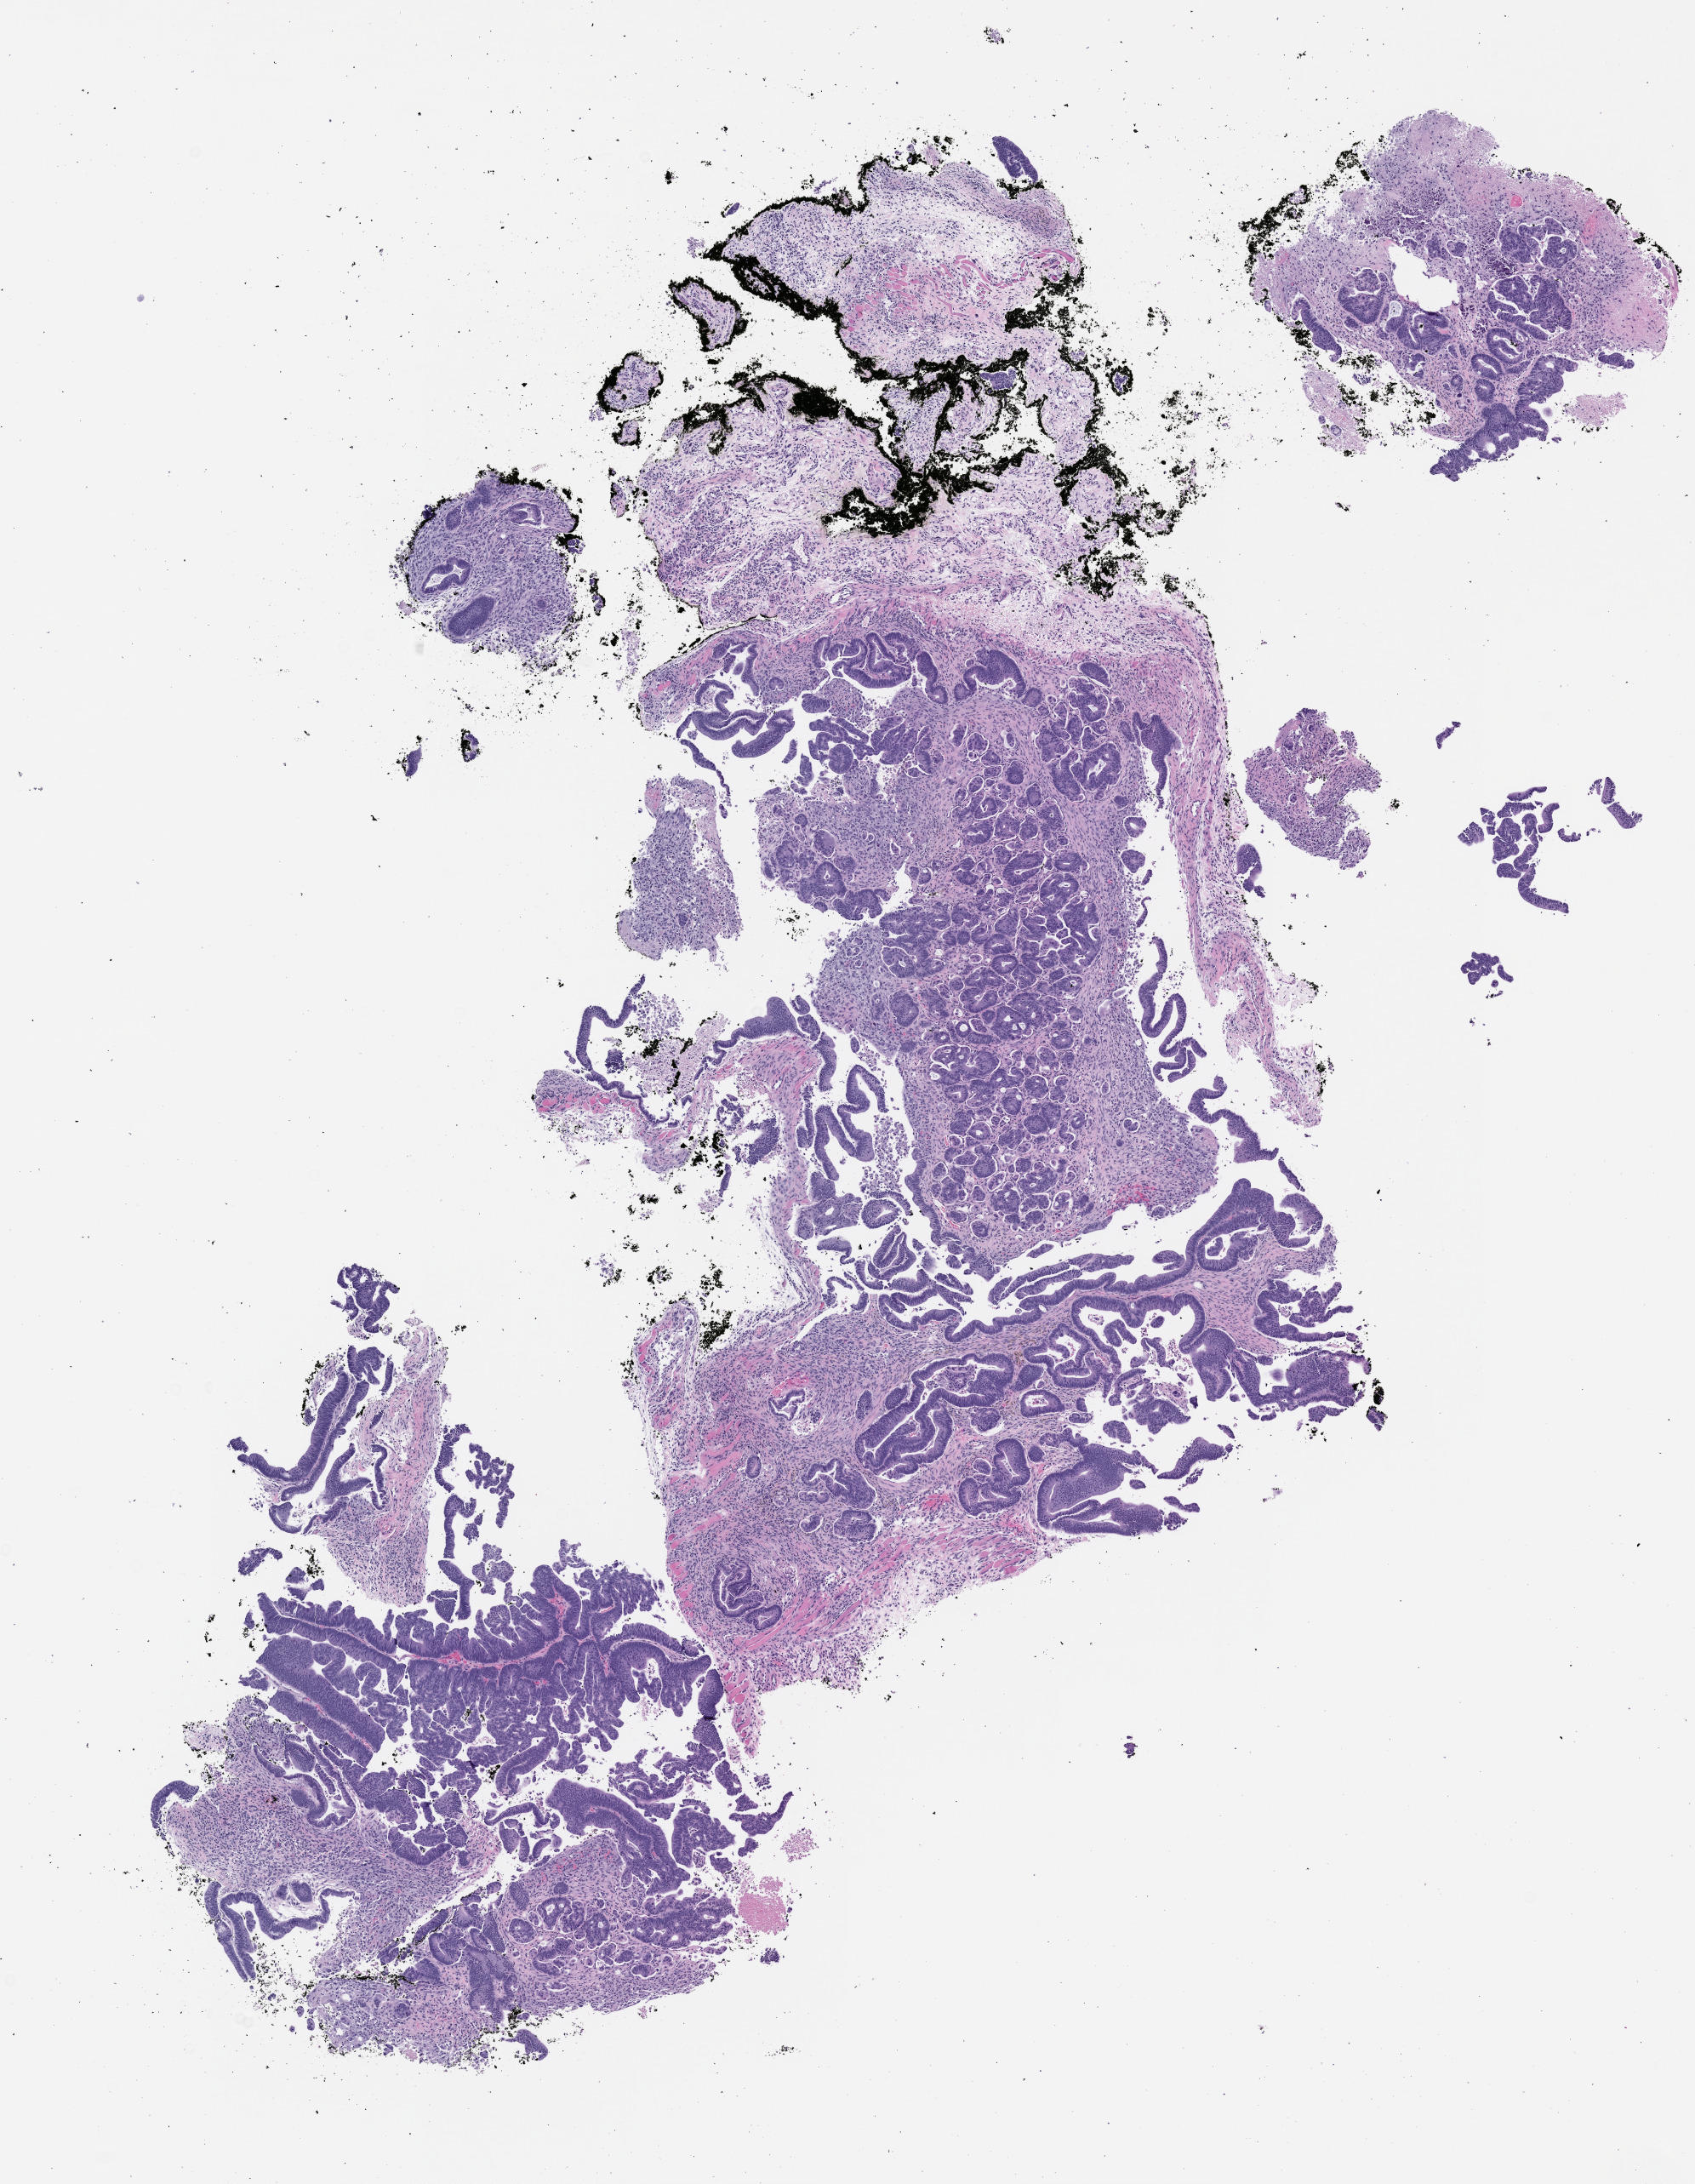
Haematoxylin and eosin whole-slide image of a patient-derived xenograft (PDX) tumor grown in a mouse, passage 1, whole scanned area (about 8.0 x 10.3 mm) shown as a low-resolution overview. Formalin-fixed, paraffin-embedded (FFPE) tissue. Tumor site category: gastrointestinal tract.
• originating patient diagnosis: Colorectal Carcinoma